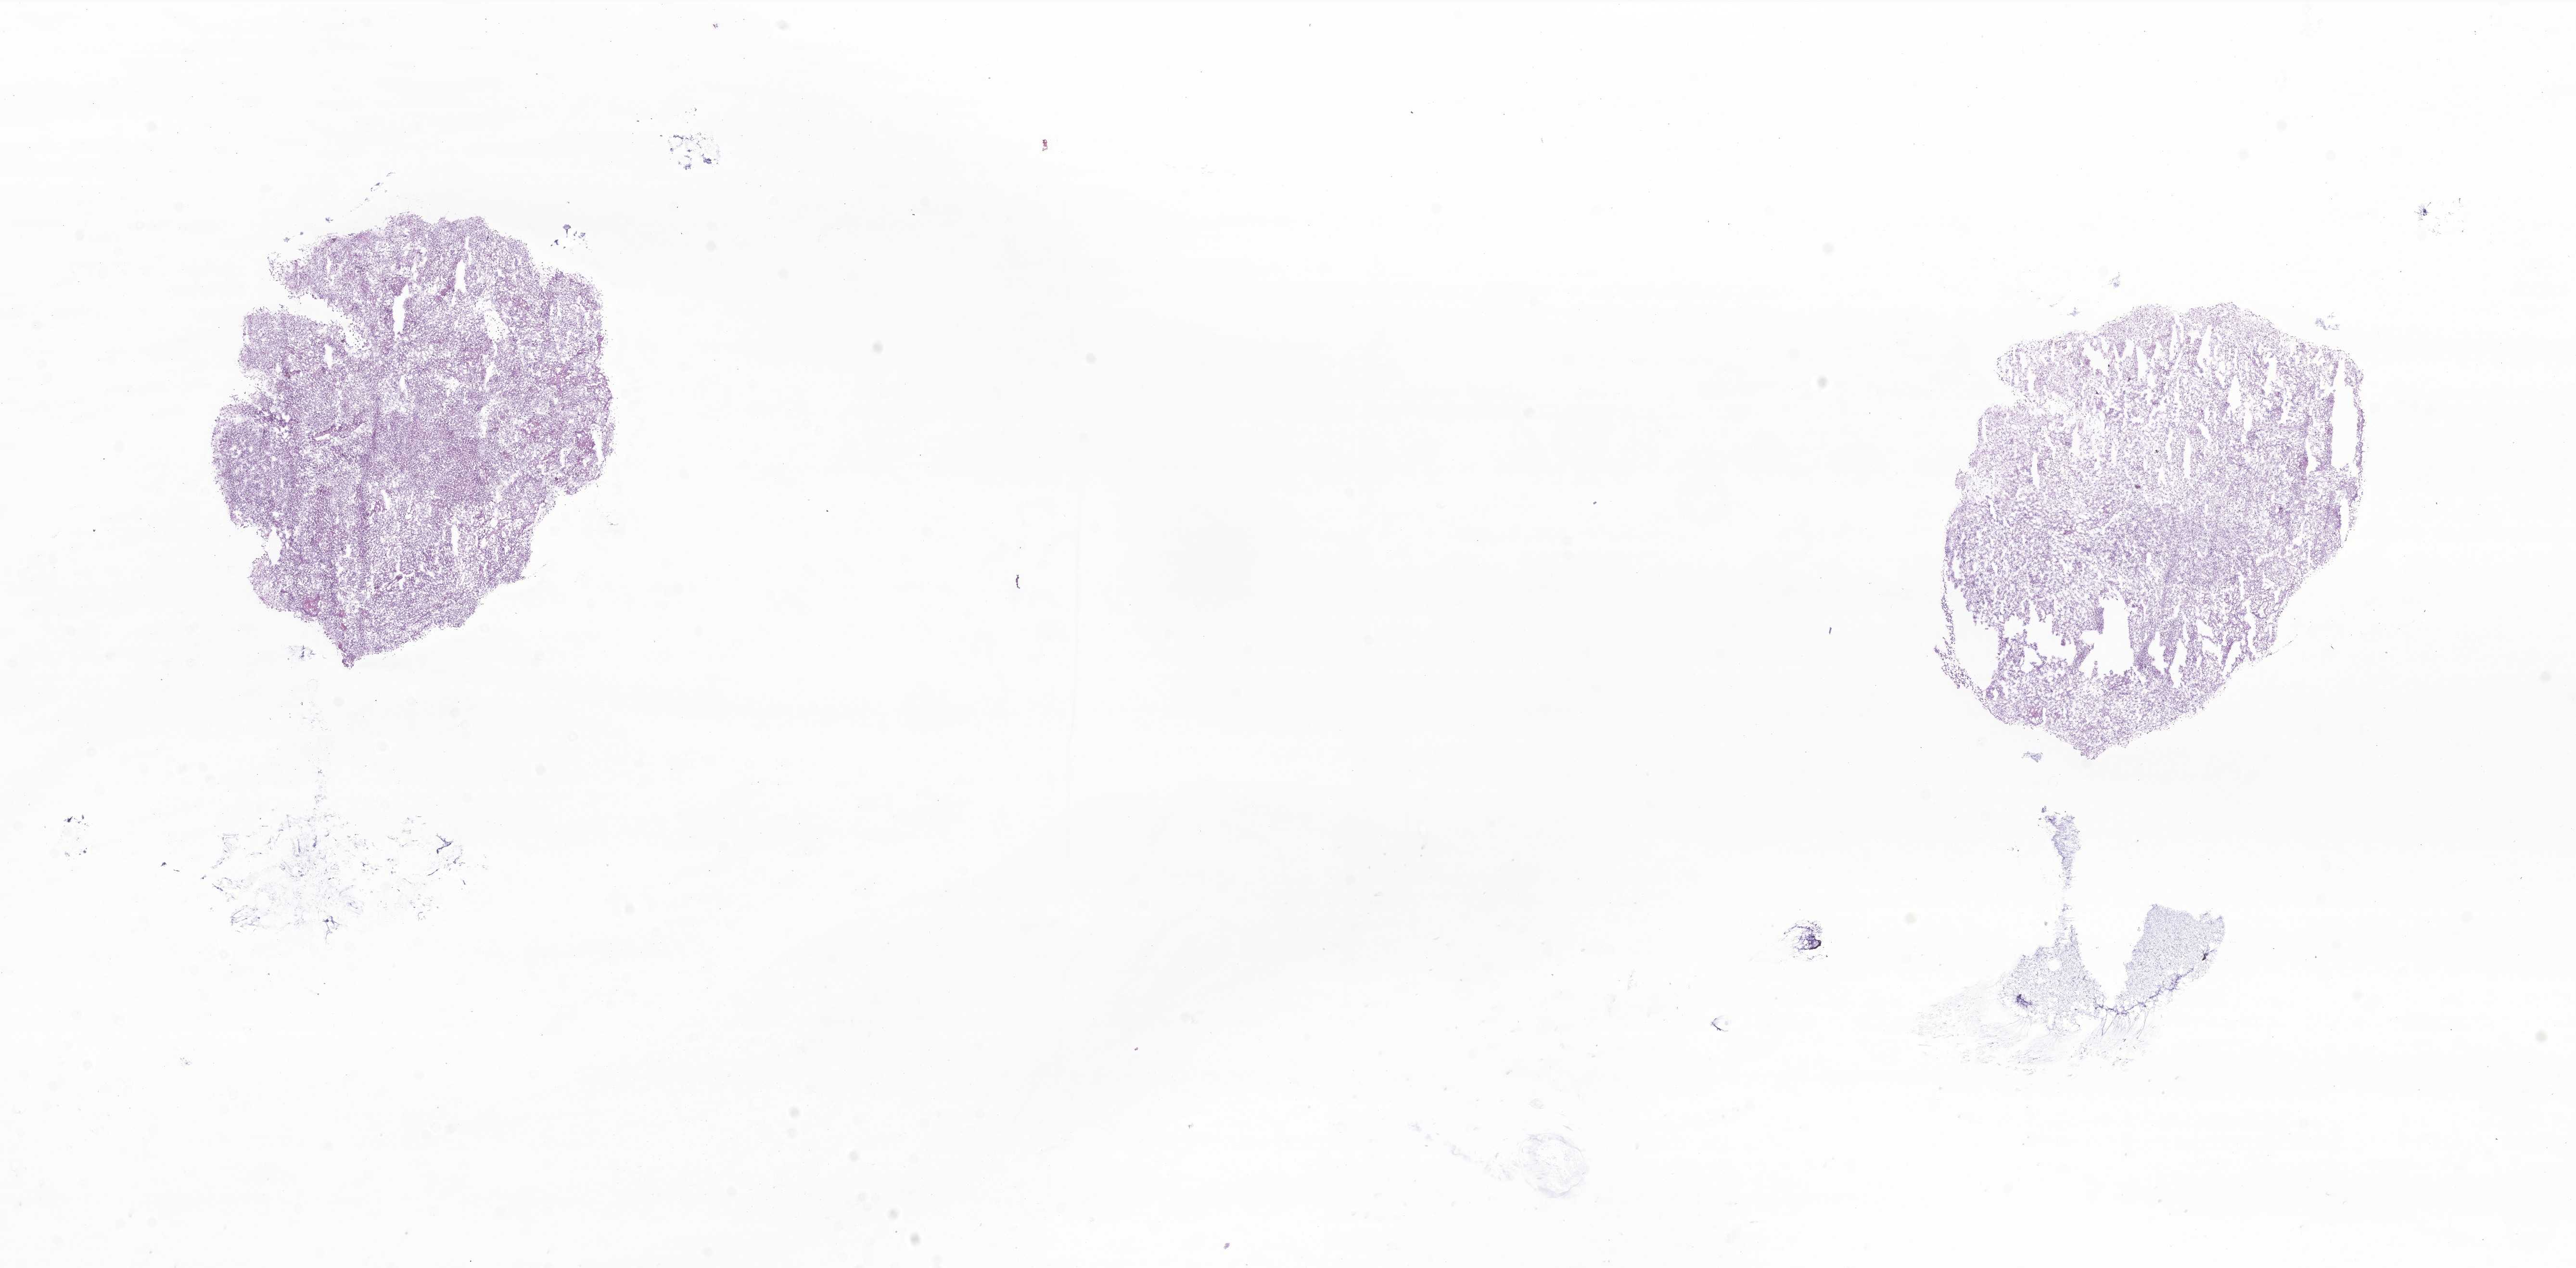
Whole-slide image, H&E stain of tumor tissue from the brain, whole scanned area (about 22.6 x 11.1 mm) shown as a low-resolution overview; frozen section. Patient male; age 168 months (14 years).
Diagnosis: Glioma, malignant.